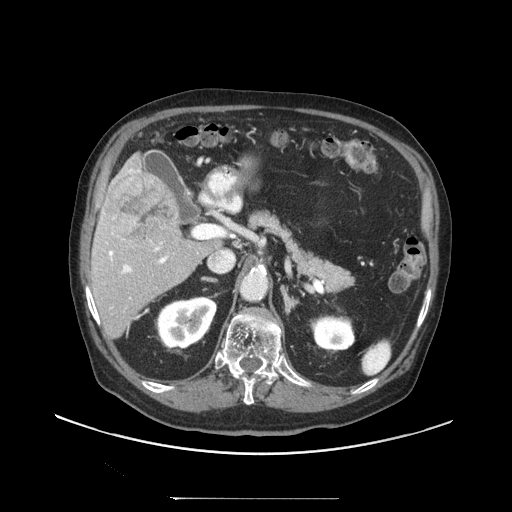
Contrast-enhanced abdominal CT (liver protocol), one axial slice; position 56 of 97 along the scan axis; 140 kVp; soft-tissue window (W 400 / L 40 HU); 2.5 mm slice thickness; 512 × 512 image matrix. From the clinical record (not read from this slice): diagnosis: hepatocellular carcinoma (patient treated with transarterial chemoembolisation; whether this scan precedes or follows treatment is not stated here); TNM stage (as recorded): Stage-IIIC; Child-Pugh class: A; tumour differentiation: well differentiated; tumour nodularity: uninodular.
Outlined on this slice (semi-automatically segmented with operator editing):
- liver parenchyma outside the tumour (the mass and vessels are separate outlines, so this box may not span the whole liver): bounding box (x1, y1, x2, y2) in pixels: (90, 153, 208, 338)
- mass: (105, 173, 178, 244)
- liver vessels: (103, 169, 168, 274)